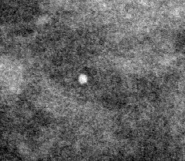
Crop from a digitized film mammogram around one marked abnormality; right breast; CC view; BI-RADS breast density category 2 (scale 1–4).
Marked abnormality: calcifications, morphology punctate; BI-RADS assessment category 2; benign; no additional work-up was recommended (benign without callback).